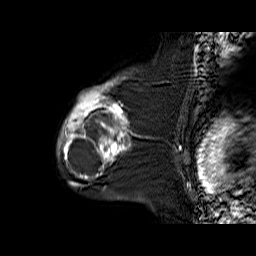
Breast MRI (dynamic contrast-enhanced), one sagittal slice. Dynamic contrast-enhanced series, time point 2 of 6 at this slice position (early post-contrast). 1.5 T. TE 6.3 ms, TR 32.9 ms. 4 mm slice thickness. 256 × 256 image matrix. Female patient. Case-level facts recorded for this patient, not image findings: setting: breast cancer imaged before/during neoadjuvant chemotherapy; receptor status: triple-negative.
Annotated regions visible in this slice (semi-automatic segmentation, software-assisted and operator-edited):
- analysis volume of interest (the breast-tissue region the enhancement analysis was run in; not a lesion): box from (x=57, y=76) to (x=145, y=170) px
- tumour enhancement mask (voxels above the 100 % enhancement threshold inside the analysis volume of interest): (x=58, y=78)–(x=128, y=170)